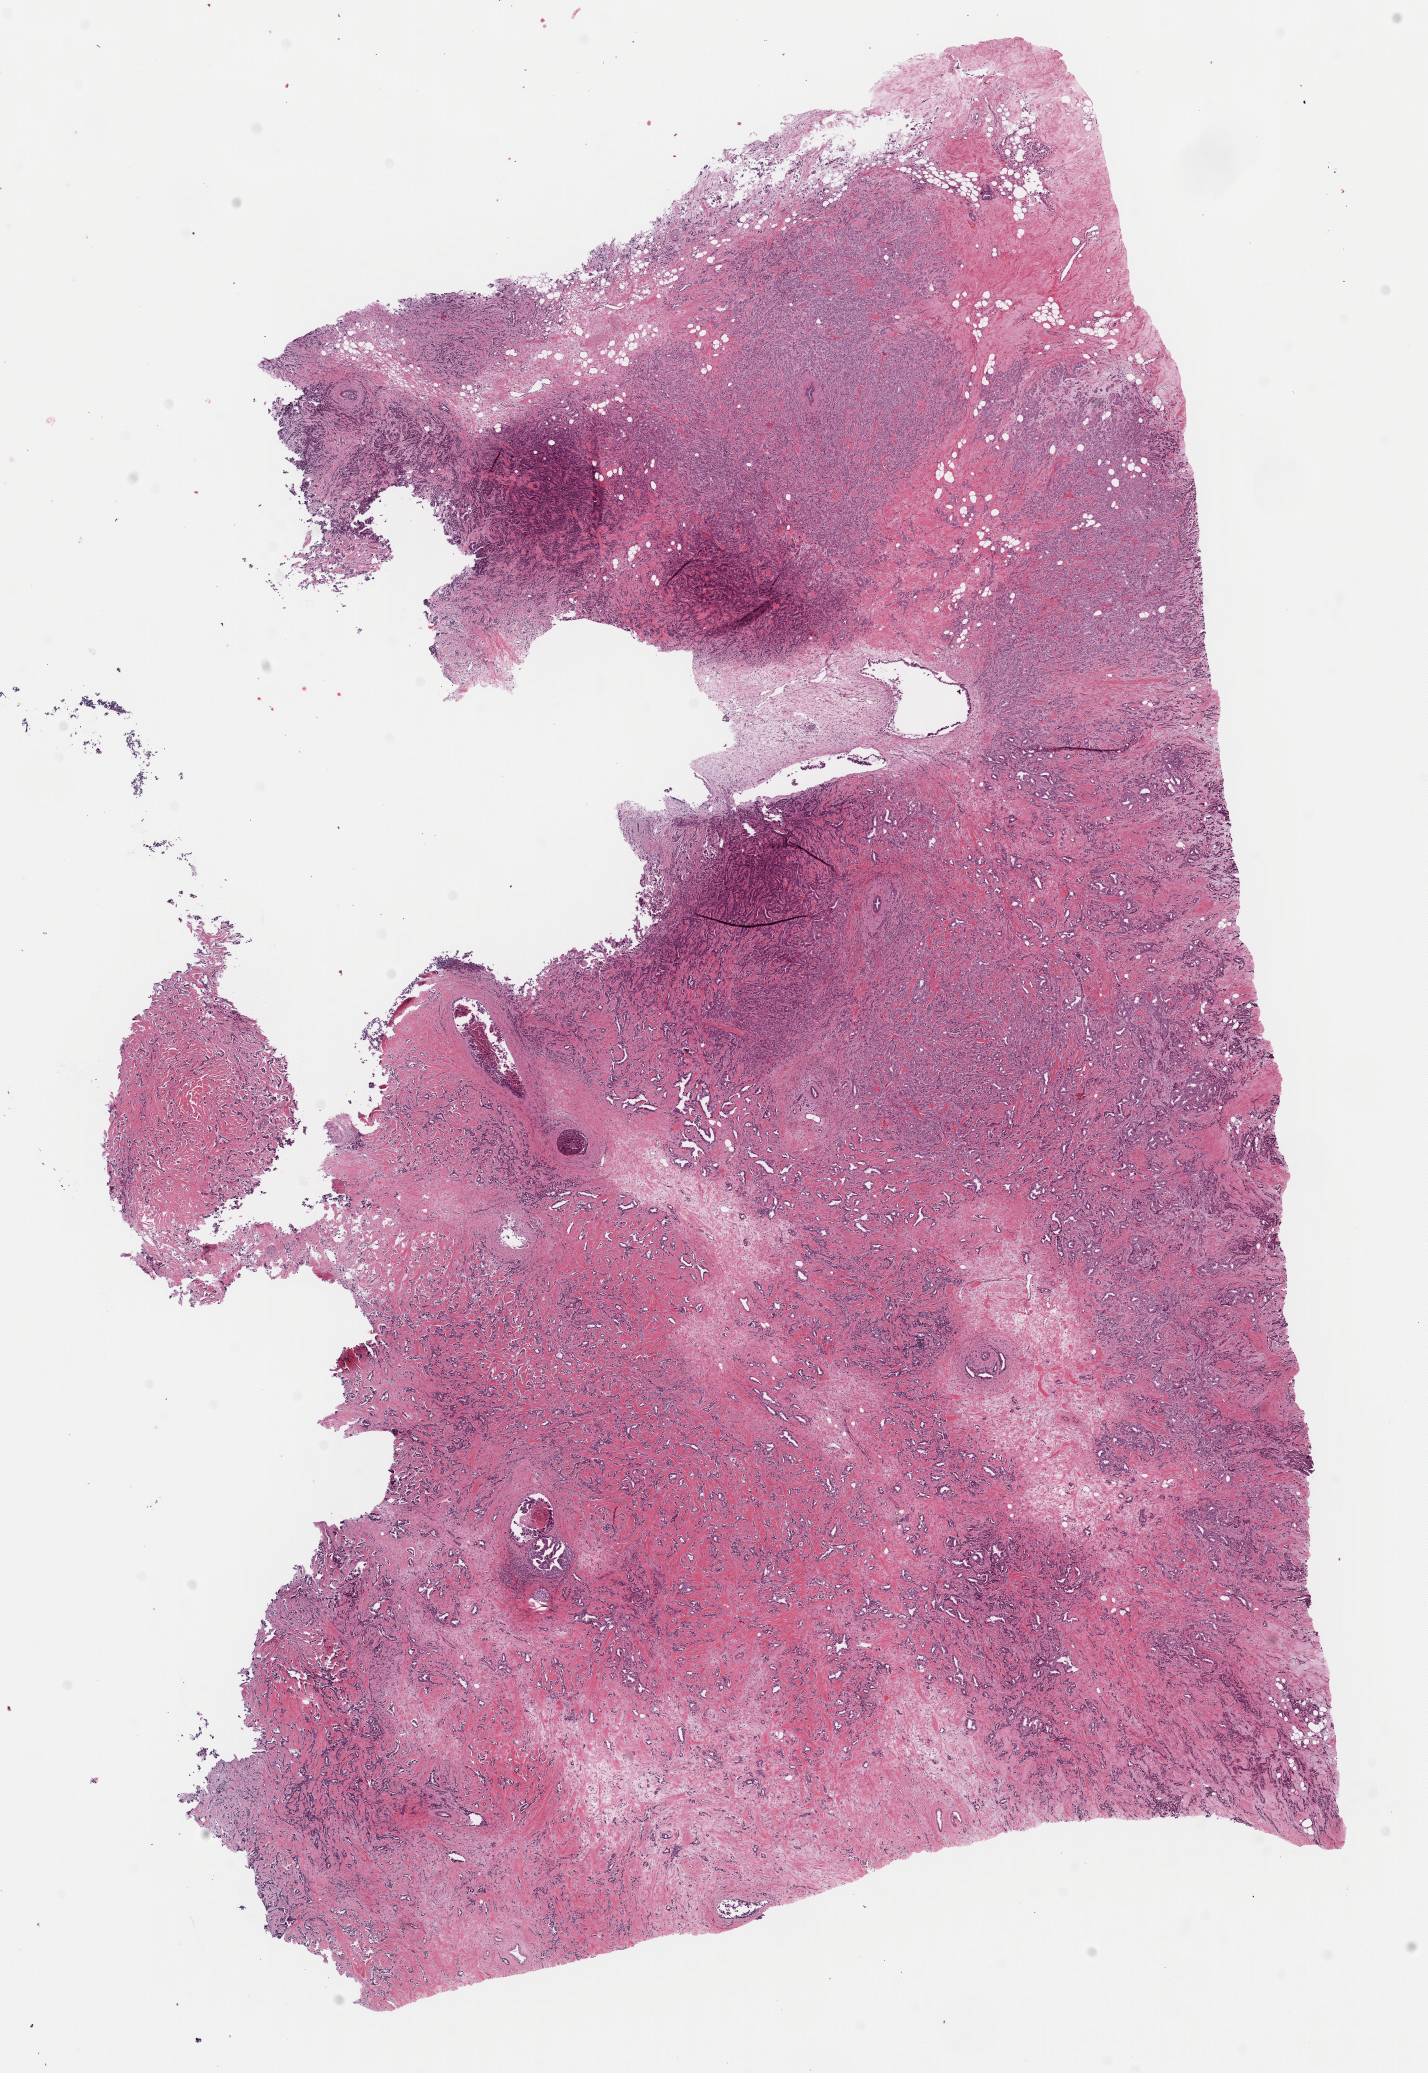
H&E-stained whole-slide image — whole scanned area (about 11.3 x 16.4 mm, acquisition: 40x scan) shown as a low-resolution overview. Formalin-fixed paraffin-embedded (FFPE) diagnostic section. Primary tumour sample from the breast. Patient: female, age at initial diagnosis 43 years.
* diagnosis: Infiltrating duct carcinoma, NOS